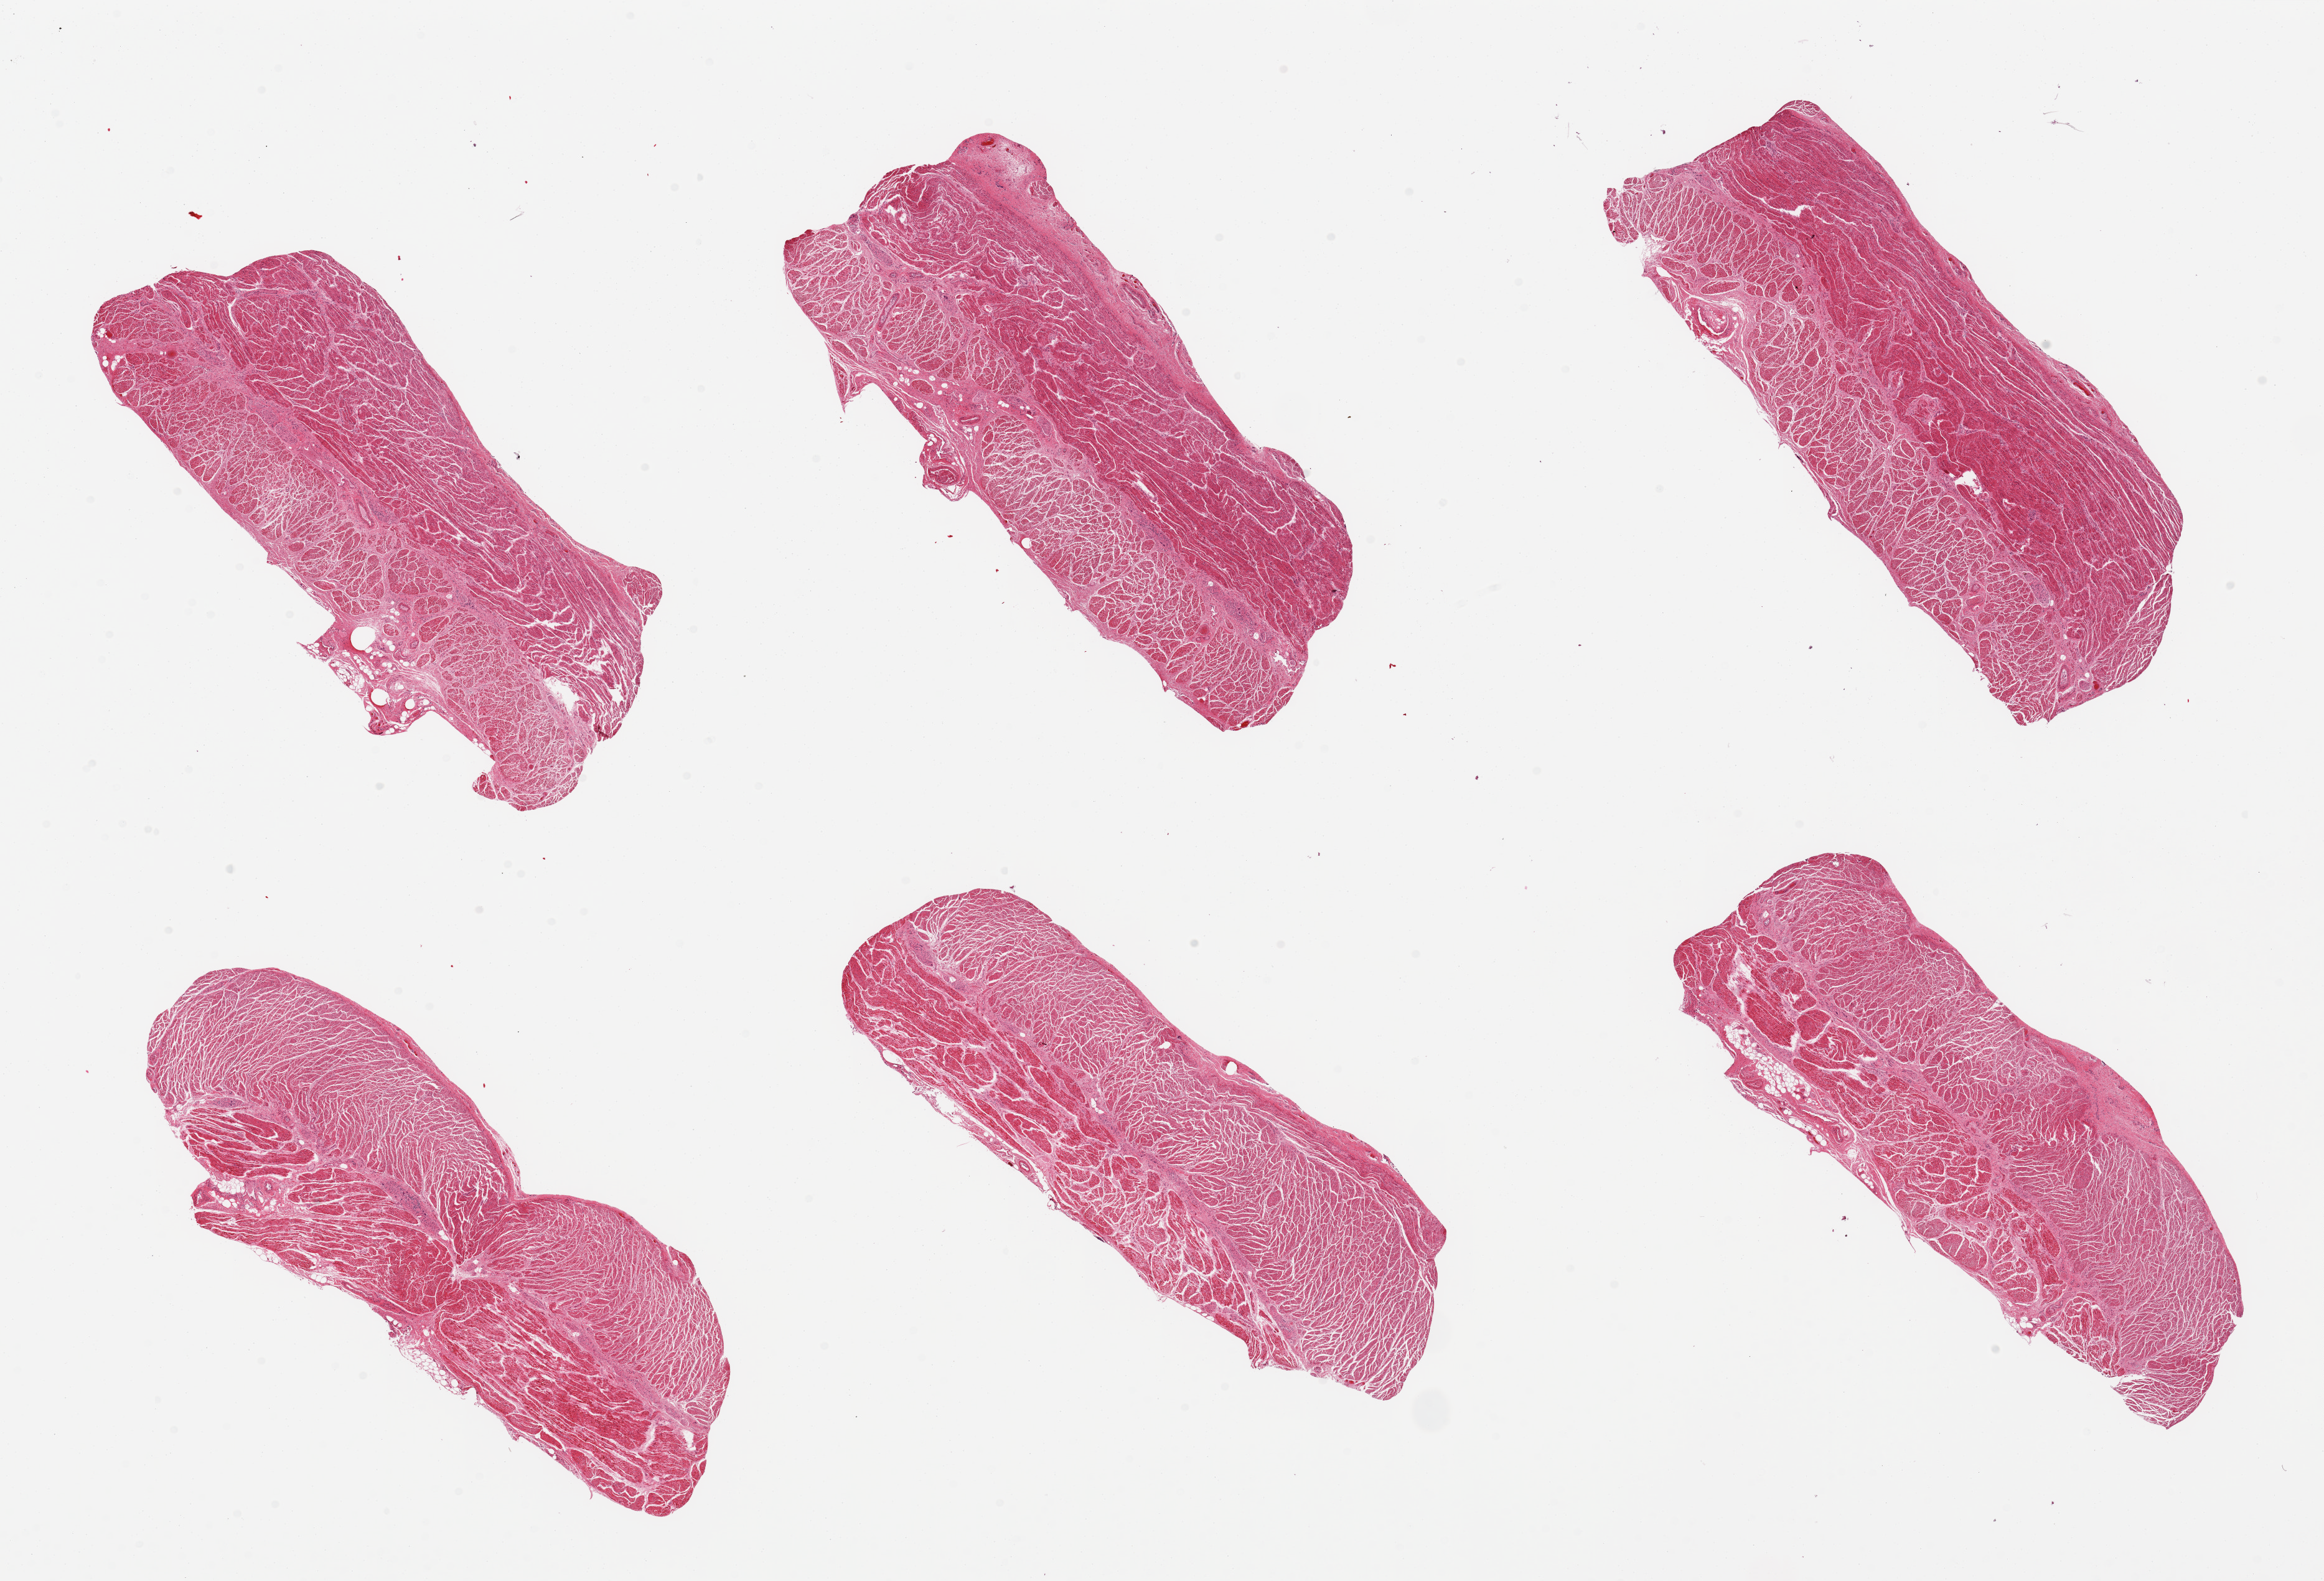
Whole-slide image, H&E stain — whole scanned area (about 29.5 x 20.1 mm) shown as a low-resolution overview; PAXgene-fixed, paraffin-embedded tissue; target tissue: gastroesophageal junction; tissue donor sample. Donor: male.
- pathologist's review note for this sample: 6 pieces, well trimmed